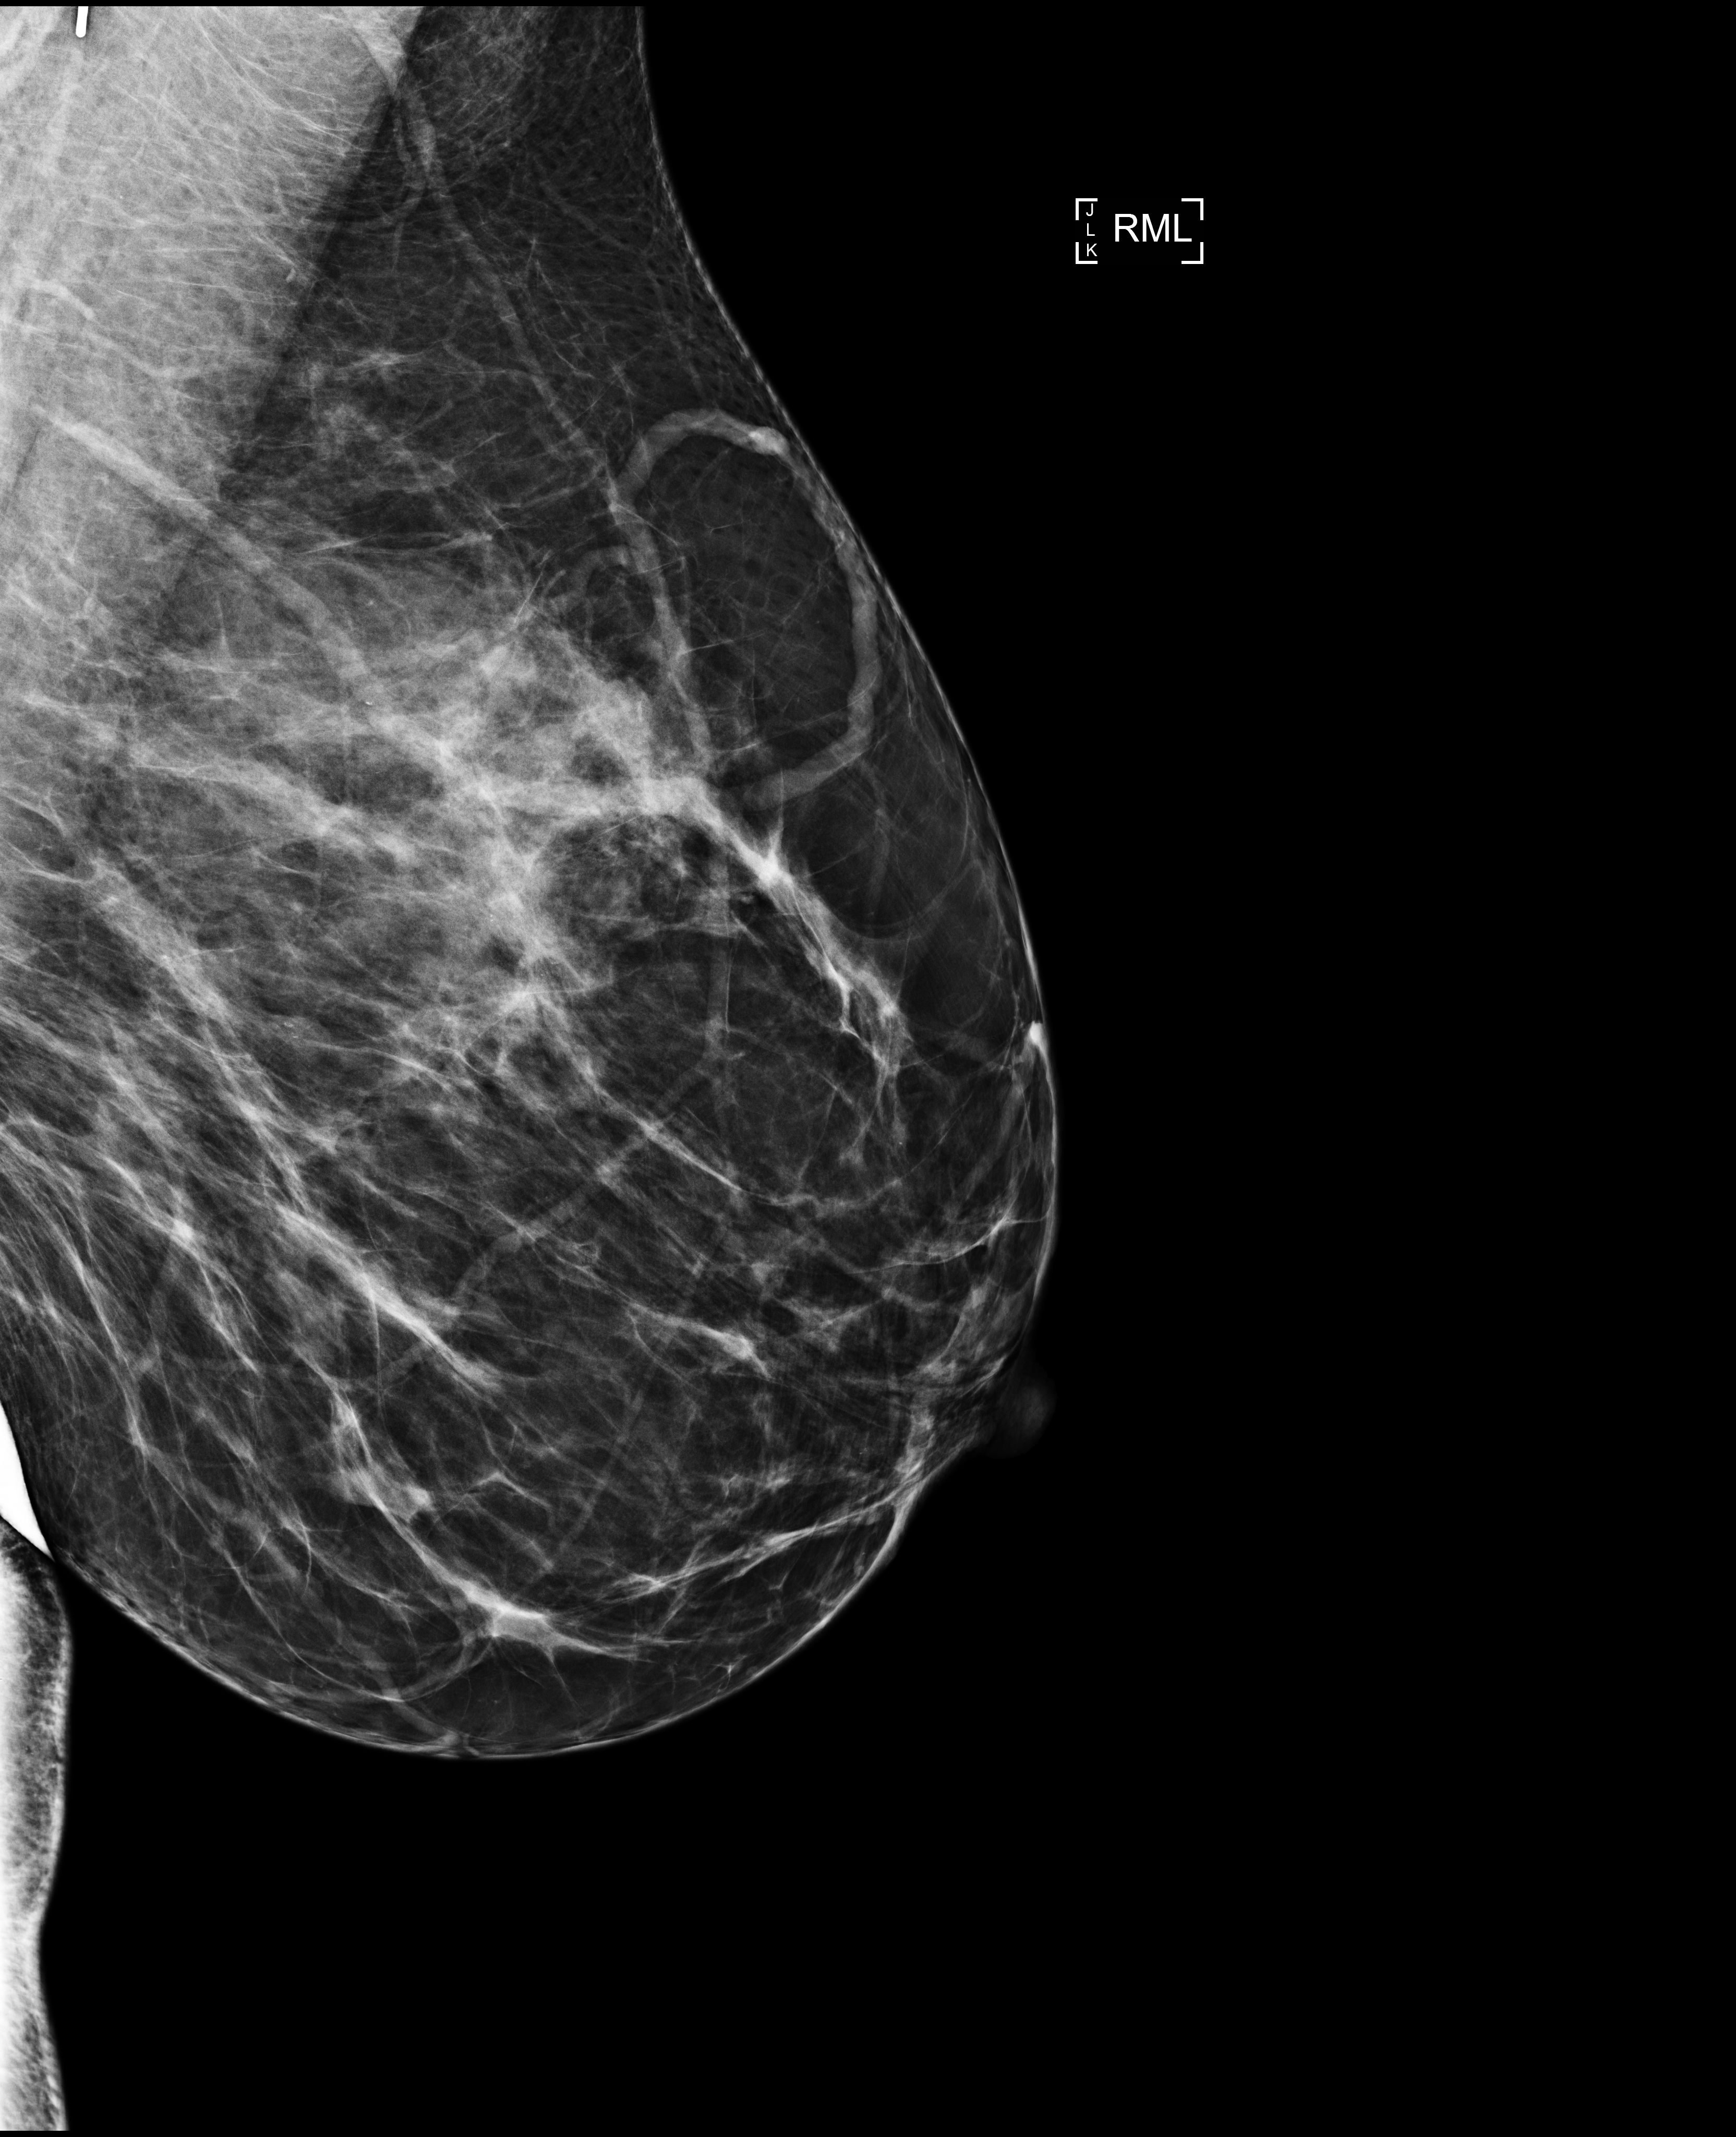
Diagnostic examination (additional views), compressed breast thickness 78 mm. Female patient, age 50 years.
Image type: full-field digital mammogram. Breast: right. Projection: mediolateral (ML) view.